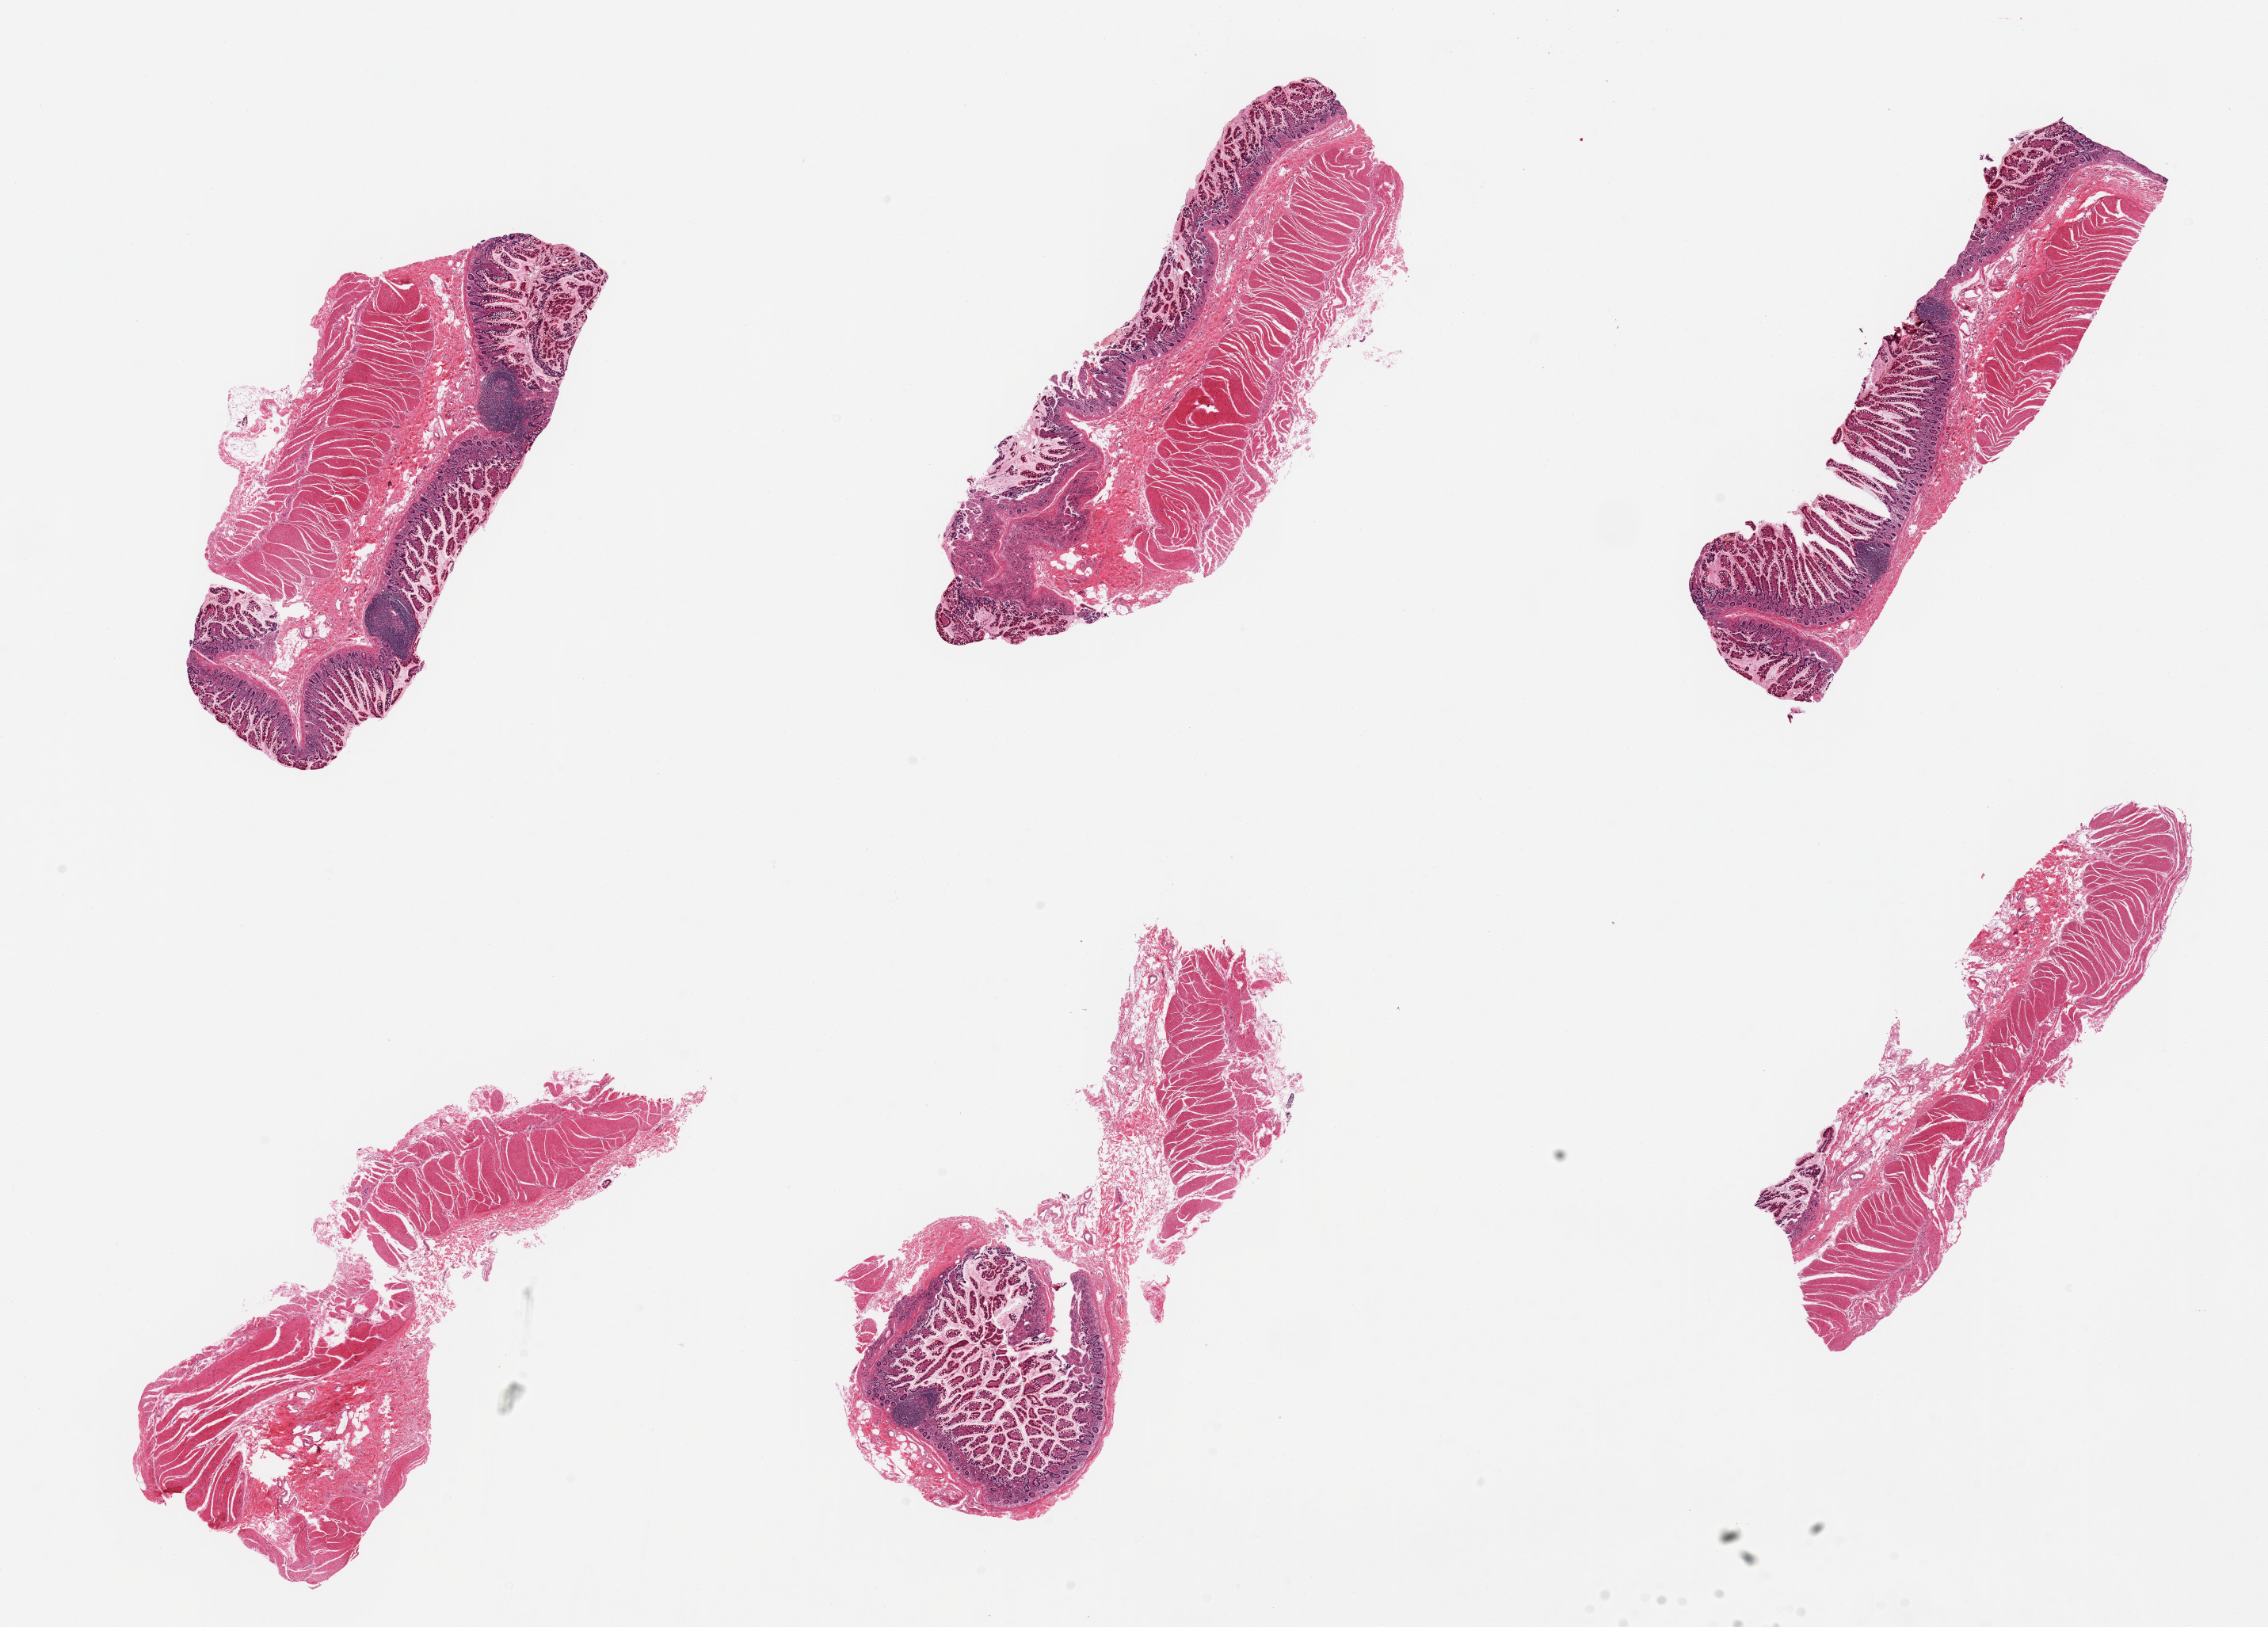
Digitized H&E-stained section — whole scanned area (about 22.6 x 16.2 mm, slide scanned at 20x) shown as a low-resolution overview, PAXgene-fixed, paraffin-embedded tissue, section of ileum (target tissue), donor tissue sample. Donor sex: male.
• review note (as recorded): 6 pieces, correct tissue but <5% target lymphoid aggregates